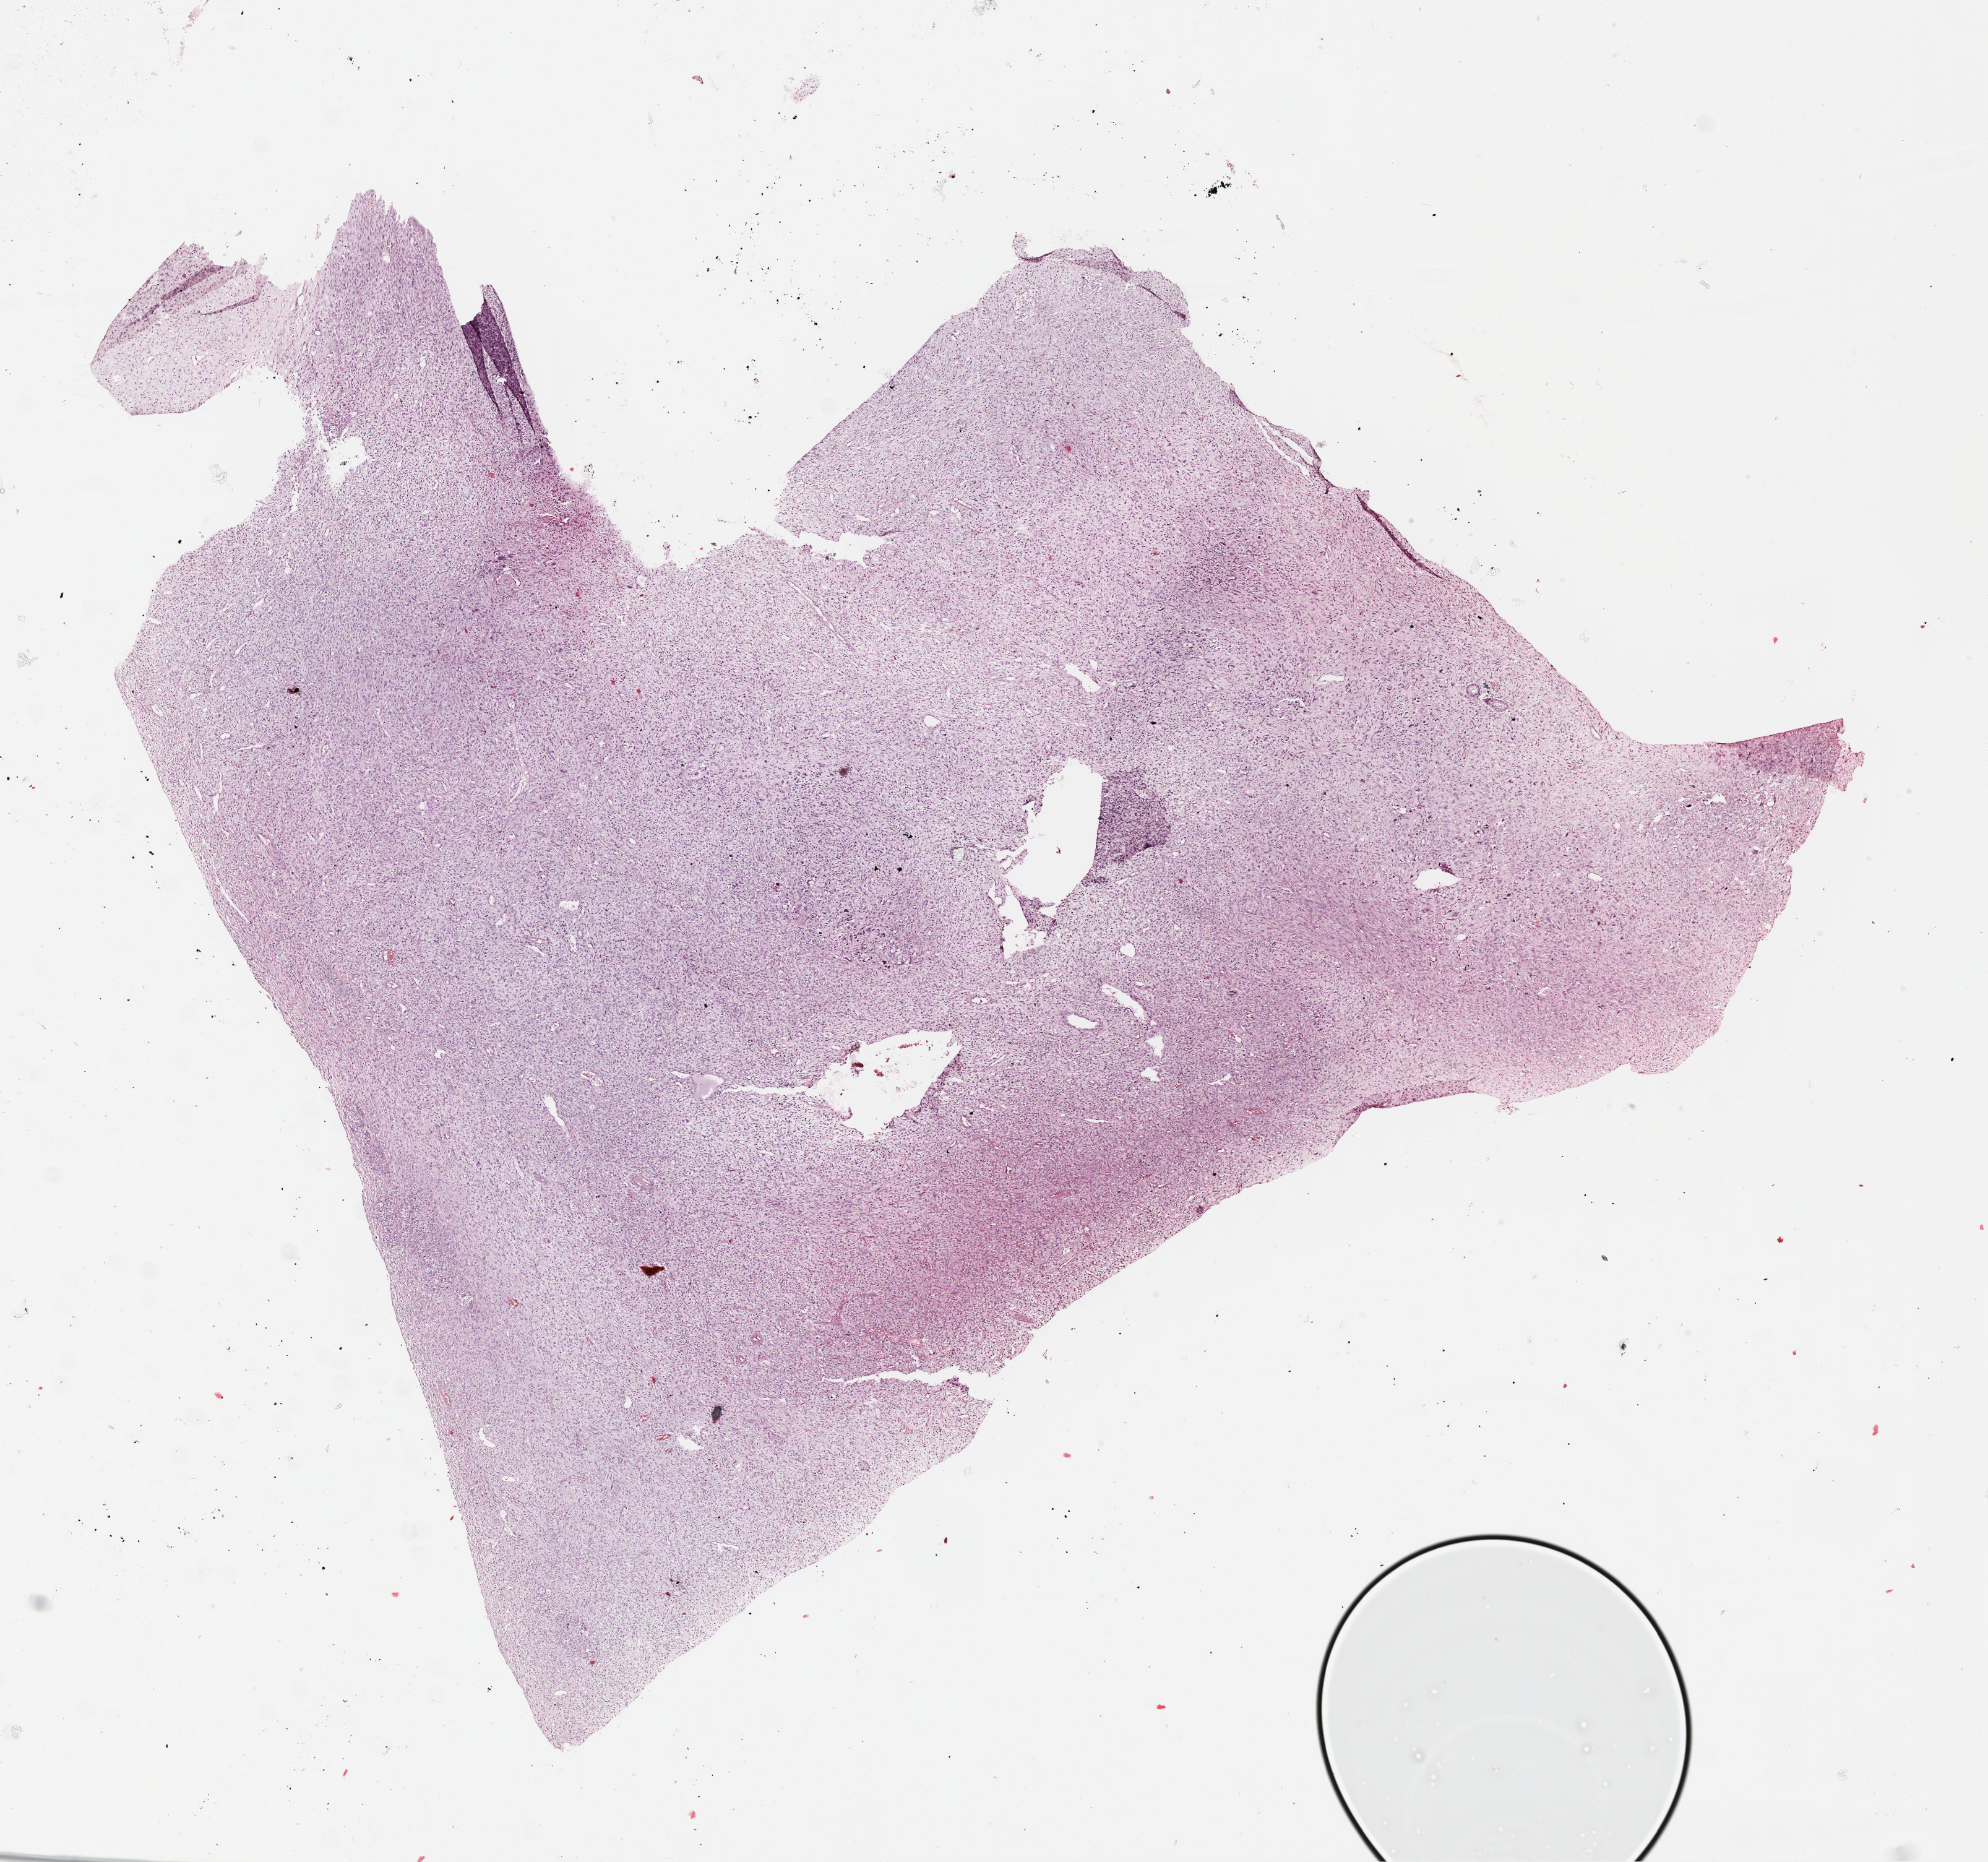
Whole-slide histology image, Hematoxylin and eosin (H&E) stained — whole scanned area (about 12.6 x 11.8 mm, acquisition: 40x scan) shown as a low-resolution overview, formalin-fixed paraffin-embedded (FFPE) diagnostic section, uterus, primary tumour sample. Female, age 55 years at initial diagnosis.
• FIGO stage: IB
• pathologic diagnosis: Mullerian mixed tumor (endometrium)